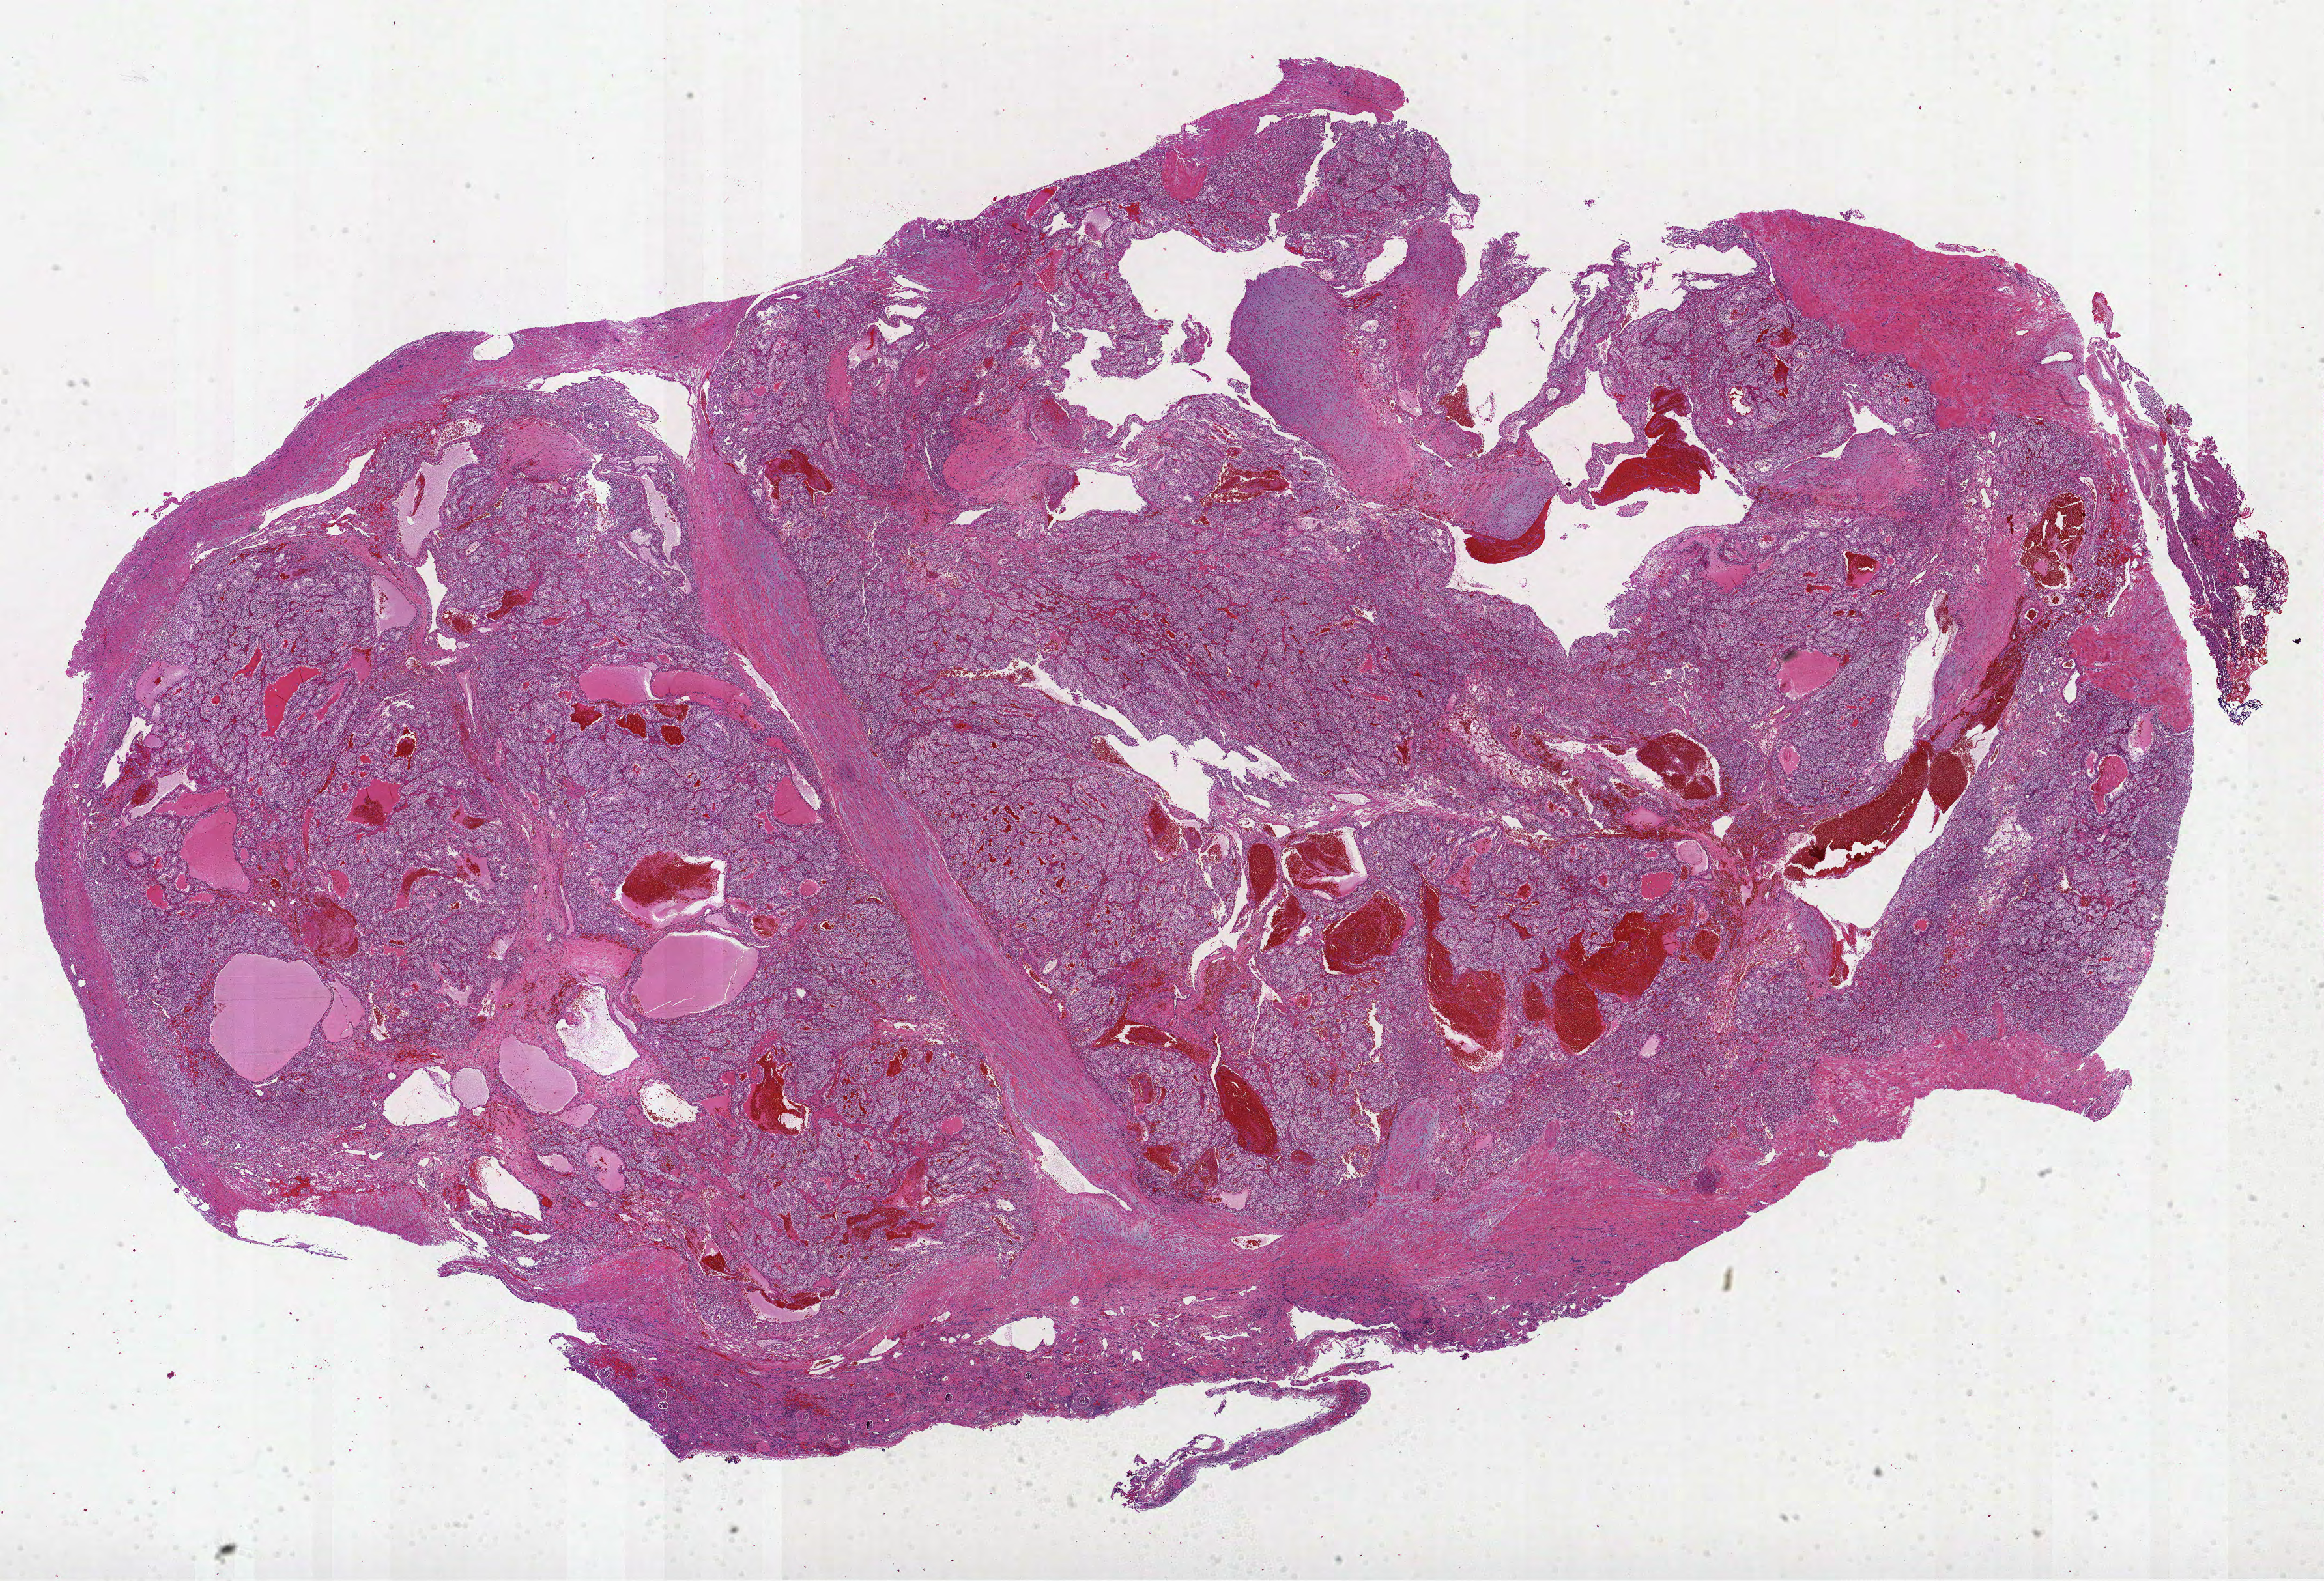
Digitized H&E-stained tissue section (whole slide), whole scanned area (about 28.8 x 19.6 mm, slide scanned at 40x) shown as a low-resolution overview; formalin-fixed paraffin-embedded (FFPE) diagnostic section; primary tumour sample from the kidney. Female, age 29 years at initial diagnosis. Histologic grade: G2 (moderately differentiated).
- pathologic diagnosis: Clear cell adenocarcinoma, NOS
- AJCC pathologic stage: I
- TNM: T1a NX M0
- laterality: right